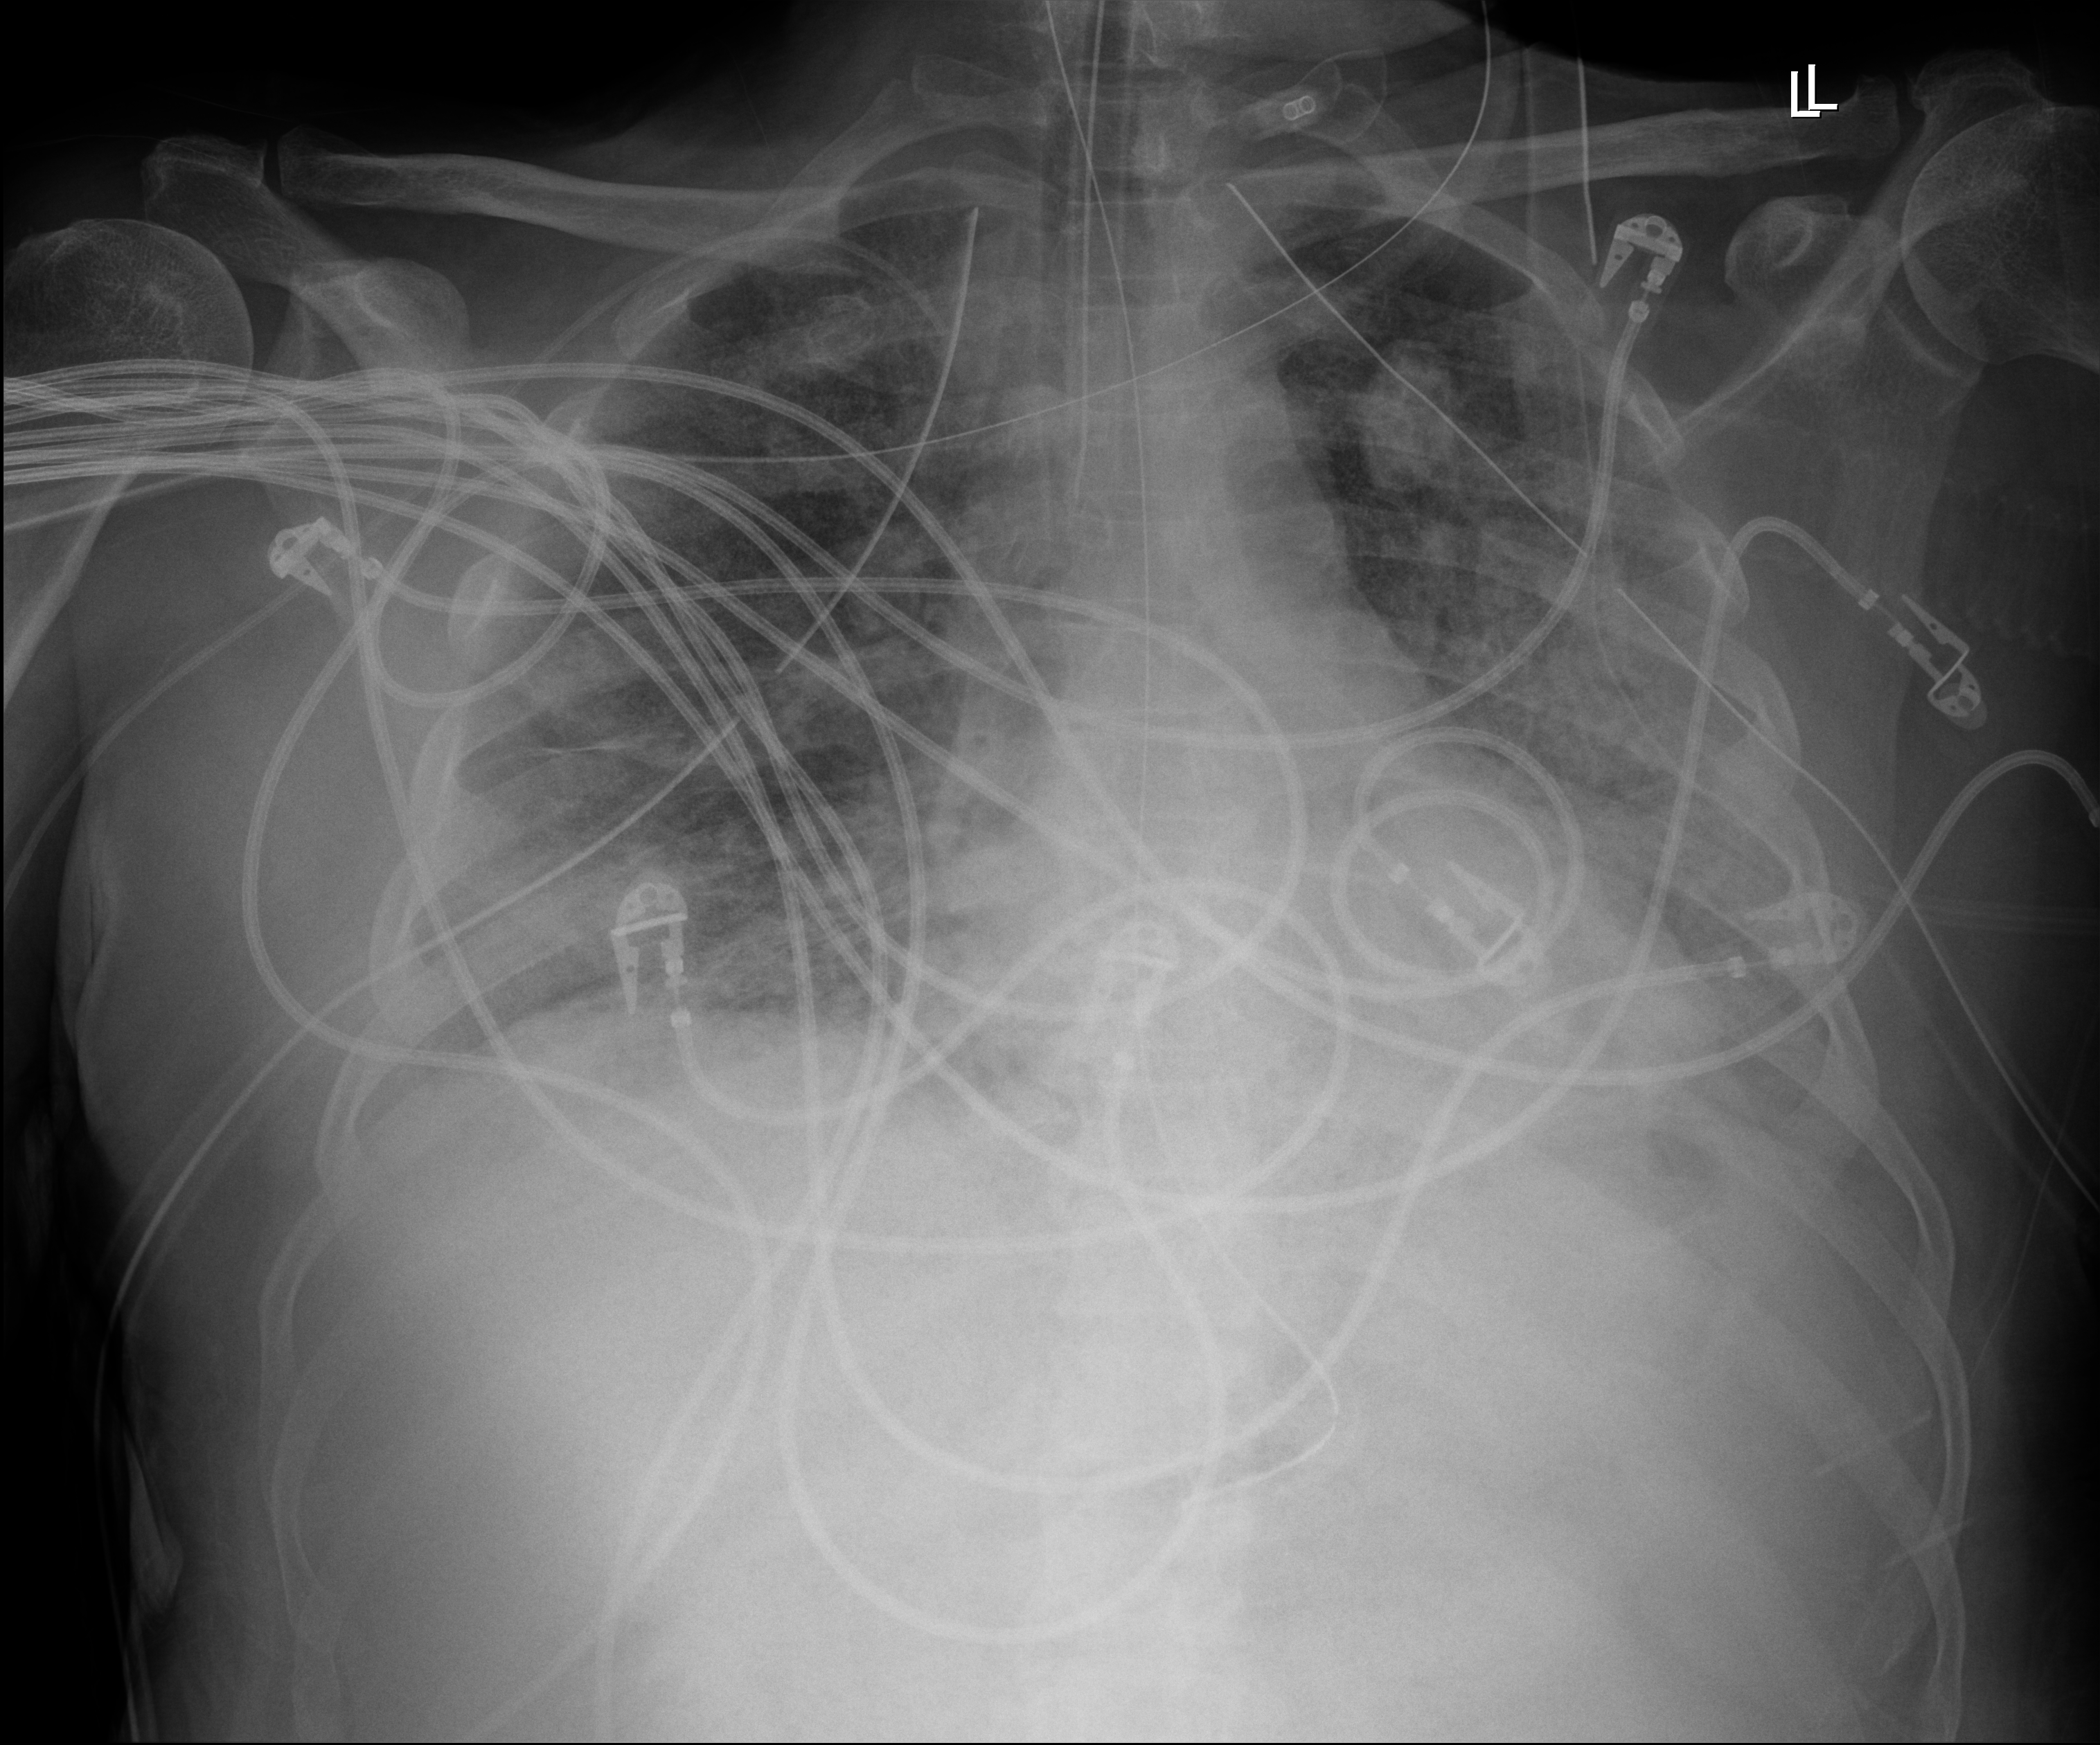
Chest X-ray (portable), anteroposterior (AP) projection. Male patient hospitalised with COVID-19, age 18–59 years.
From the hospital-stay record, not from the radiograph (when in the stay this image was taken is not recorded):
- mechanically ventilated during this hospital stay: yes
- length of hospital stay: 83 days
- admitted to intensive care during this hospital stay: yes